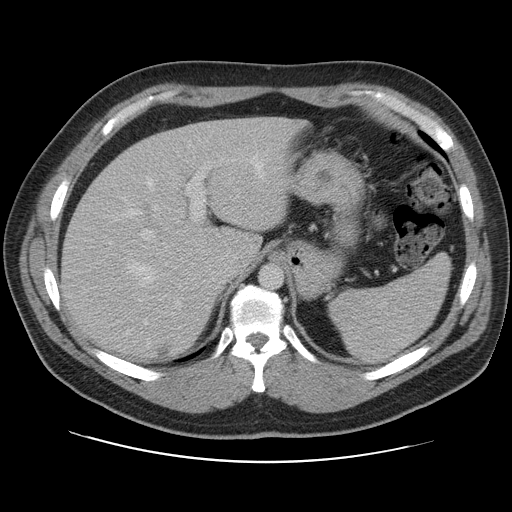
Contrast-enhanced abdominal CT, one axial slice; position 80 of 109 along the scan axis; intravenous contrast given; soft-tissue window (W 400 / L 40 HU); 512 × 512 image matrix, field of view 402 × 402 mm. Male patient, age 35 years. Case-level facts recorded for this patient, not image findings: diagnosis: colorectal cancer liver metastases, imaged before liver resection; multiple liver metastases: yes; largest metastasis: 2.8 cm; disease in both lobes: yes.
Annotated regions visible in this slice (expert manual segmentation):
- hepatic veins: bounding box <117,153,264,325> (left, top, right, bottom; pixels)
- liver: <62,118,298,359>
- planned liver remnant (the part of the liver to remain after resection): <62,118,289,357>
- portal vein (with intrahepatic branches): <107,160,215,302>
- liver metastasis: <157,348,170,358>